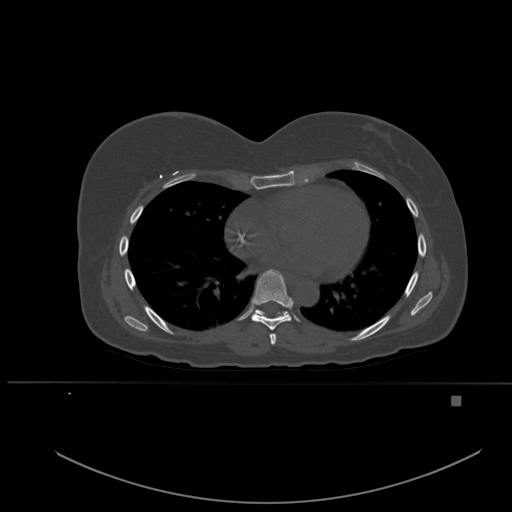
CT including the spine, one axial slice; position 333 of 651 along the scan axis; bone window (W 1800 / L 400 HU); 1.5 mm slice thickness; 512 × 512 image matrix, field of view 443 × 443 mm. Female patient, age 49 years. Case-level facts recorded for this patient, not image findings: primary cancer: breast.
Annotated regions visible in this slice (semi-automatic segmentation, software-assisted and operator-edited):
- T6 vertebra: bounding box [x1, y1, x2, y2] px = [270, 333, 276, 345]
- T7 vertebra: [251, 269, 294, 330]
- T8 vertebra: [255, 309, 288, 317]